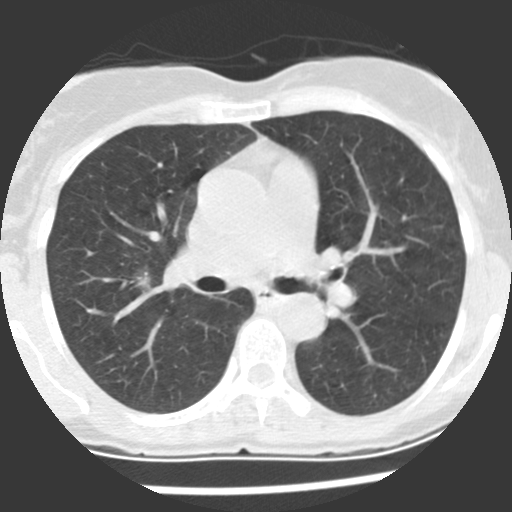
Low-dose screening chest CT, axial slice, baseline annual screen, lung window (W 1500 / L -600 HU), 2.5 mm slice thickness, slice 96 of 225 in the series, 512 × 512 image matrix. Female participant, aged 60 years at enrolment. Current smoker at enrolment.
• Lesion marked by an expert reader, bounding box (x1, y1, x2, y2) in pixels: (114, 258, 171, 305).
• The screening reader recorded 2 non-calcified nodules or masses ≥4 mm on this exam (right upper lobe, right middle lobe); which of them this box marks is not recorded.
• Official screen result: positive, change unspecified: nodule(s) >= 4 mm or enlarging nodule(s), mass(es), or other non-specific abnormalities suspicious for lung cancer.
• Lung cancer was diagnosed 10 days after this screen: adenocarcinoma, NOS, right upper lobe, stage IIIA (AJCC 6th edition), 20 mm at pathology.